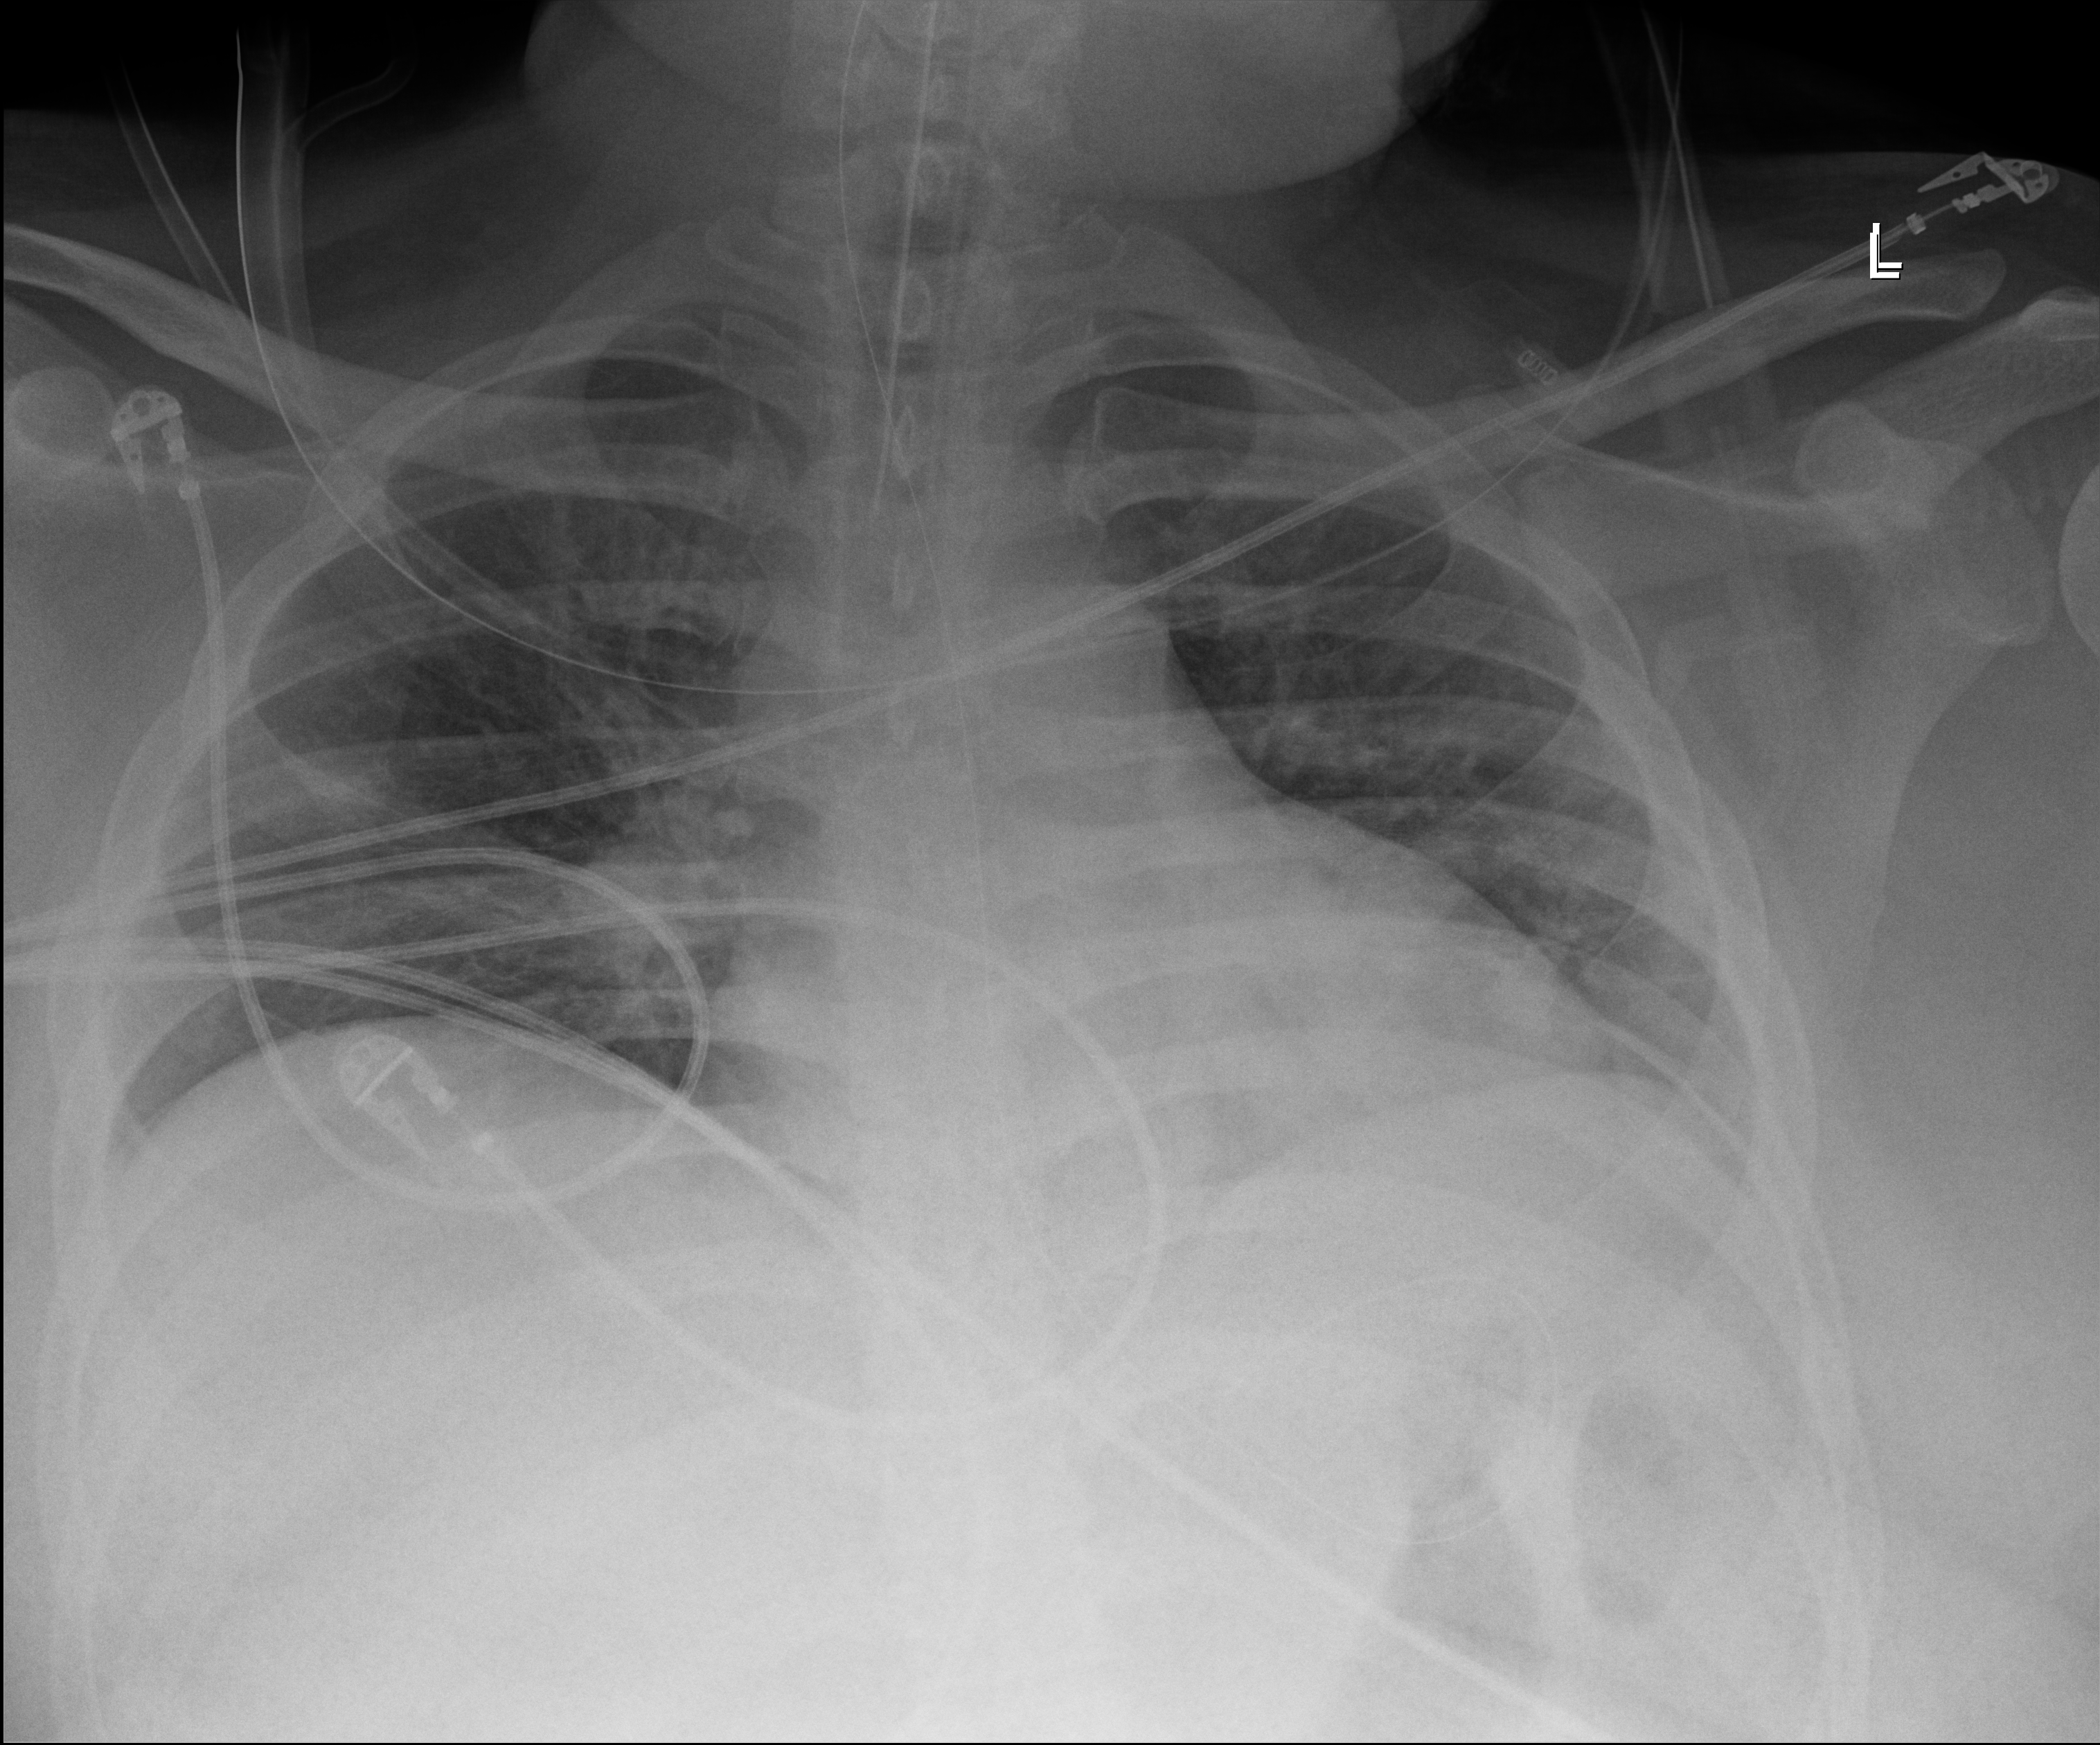
Chest X-ray (portable); anteroposterior (AP) projection. Male patient hospitalised with COVID-19, age 18–59 years.
From the hospital-stay record, not from the radiograph (when in the stay this image was taken is not recorded):
- mechanically ventilated during this hospital stay: yes
- hypertension (admission record): no